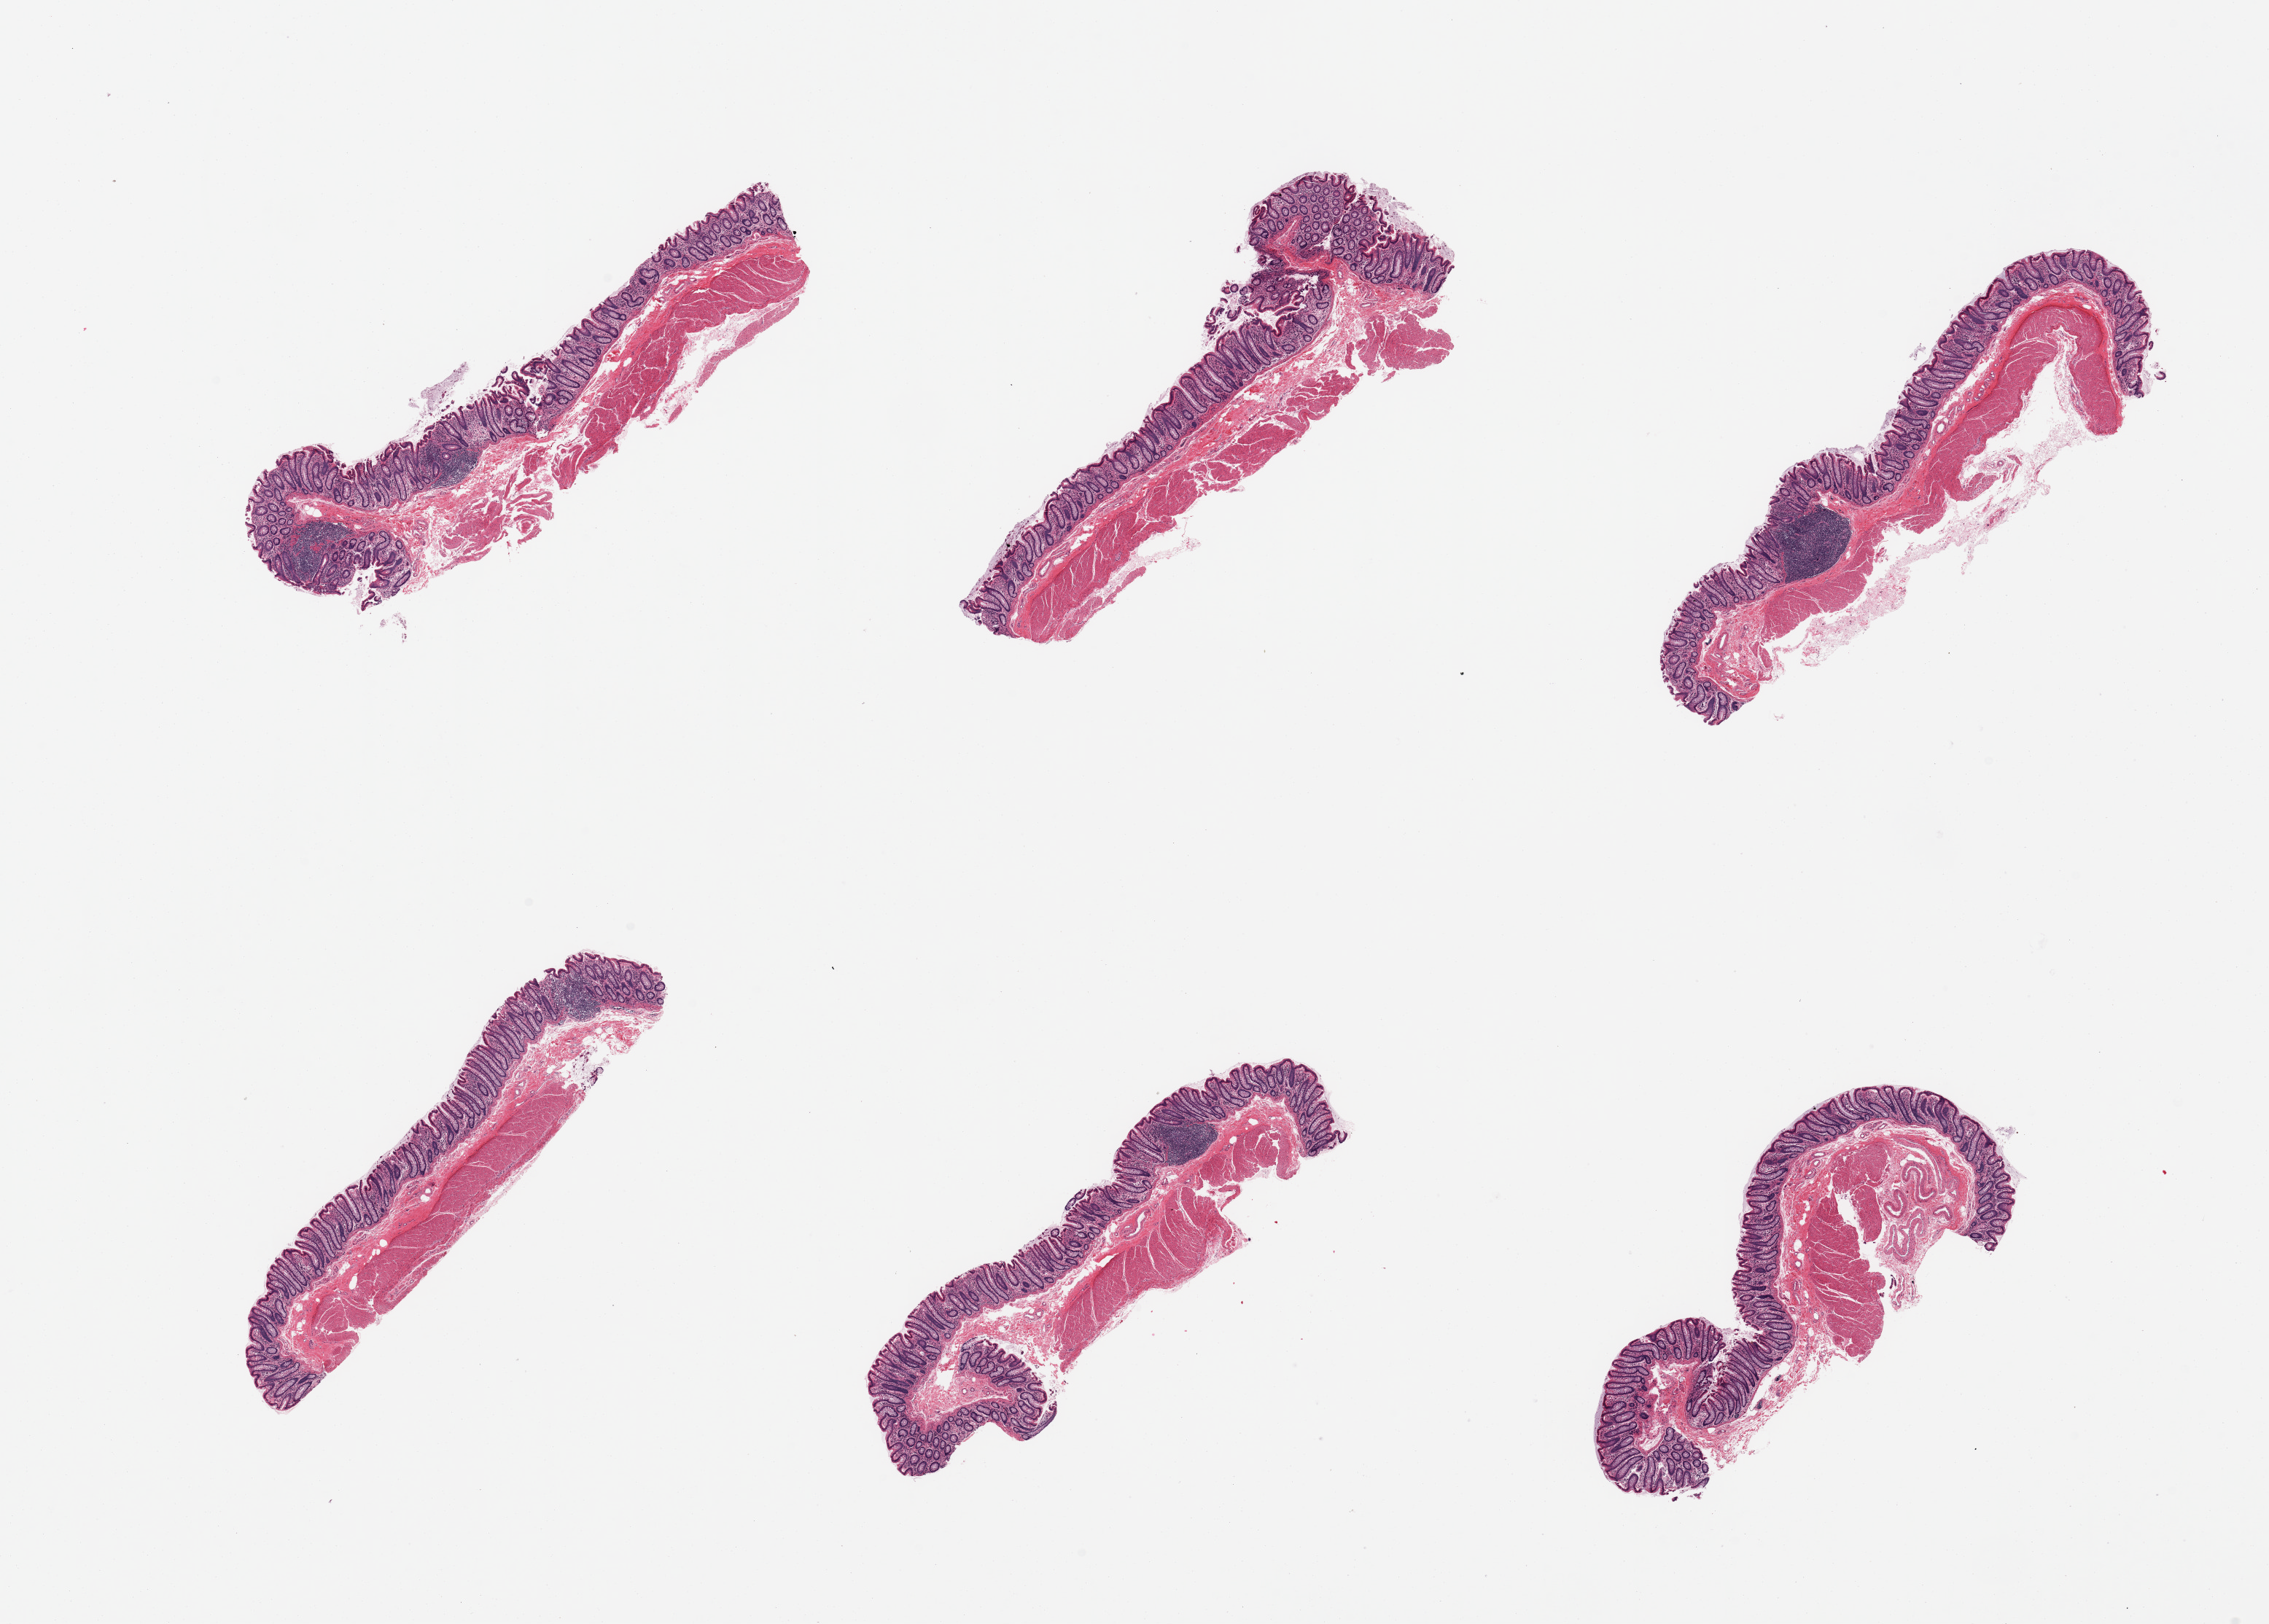
H&E whole-slide image, brightfield — shown as a low-resolution overview of the whole scanned area (about 24.6 x 17.6 mm, acquisition: 20x scan). PAXgene-fixed, paraffin-embedded tissue. Section of transverse colon (target tissue). Donor tissue sample. Female donor.
Reviewer comment on this tissue sample: 6 pieces; well dissected; well preserved.